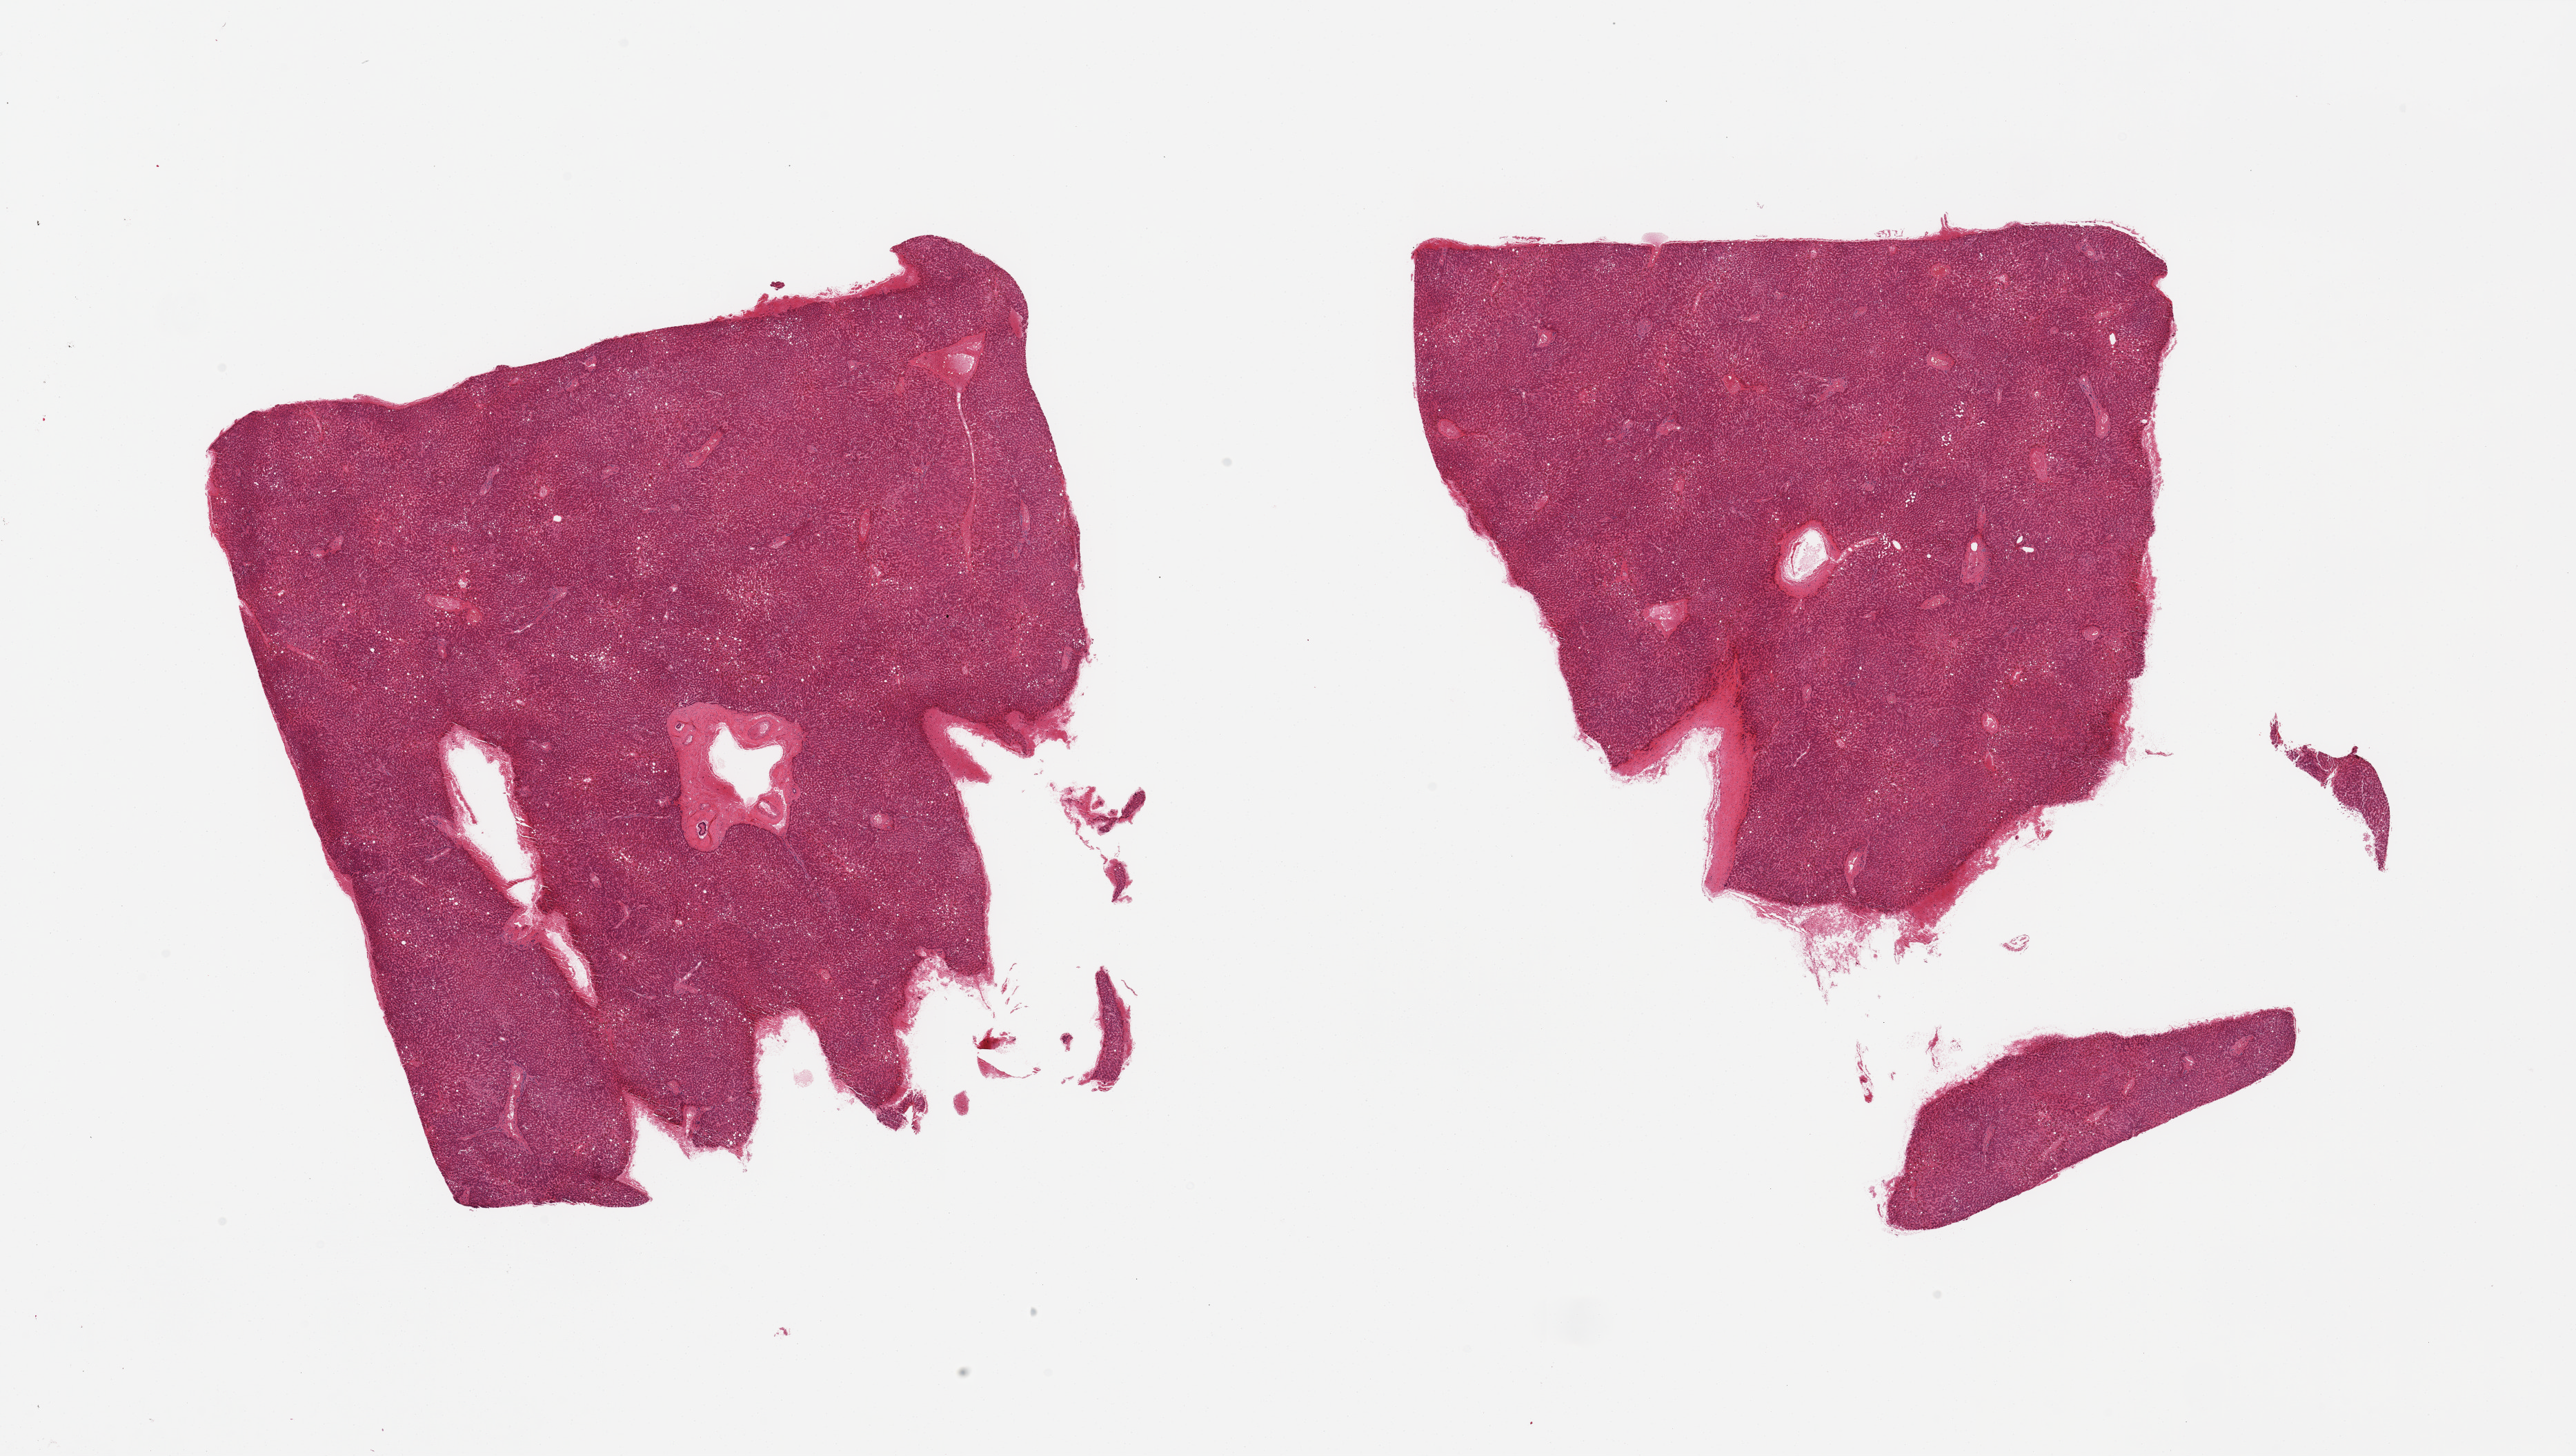
Digitized hematoxylin and eosin (H&E)-stained section, brightfield, whole scanned area (about 29.5 x 16.7 mm) shown as a low-resolution overview, PAXgene-fixed paraffin-embedded (PFPE) section, sampled site (target tissue): liver, tissue donor sample. Donor: male.
Review note (as recorded): 3 pieces; mild steatosis.